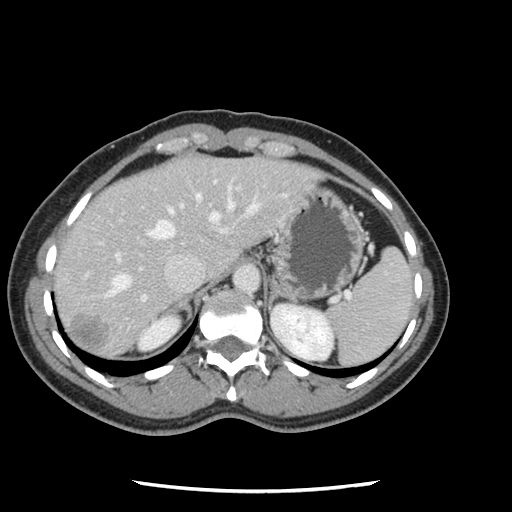
Contrast-enhanced abdominal CT, one axial slice. Position 92 of 134 along the scan axis. 120 kVp. Intravenous contrast given. Soft-tissue window (W 400 / L 40 HU). 2.5 mm slice thickness. 512 × 512 image matrix, field of view 330 × 330 mm. Female patient, age 43 years. From the clinical record (not read from this slice): diagnosis: colorectal cancer liver metastases, imaged before liver resection; multiple liver metastases: yes; largest metastasis: 3.4 cm.
Annotated regions visible in this slice (outlined manually by an expert reader):
- hepatic veins: box from (x=106, y=193) to (x=261, y=297) px
- liver: (x=55, y=157)–(x=317, y=359)
- planned liver remnant (the part of the liver to remain after resection): (x=55, y=161)–(x=192, y=309)
- portal vein (with intrahepatic branches): (x=83, y=180)–(x=231, y=302)
- liver metastasis: (x=70, y=316)–(x=109, y=354)